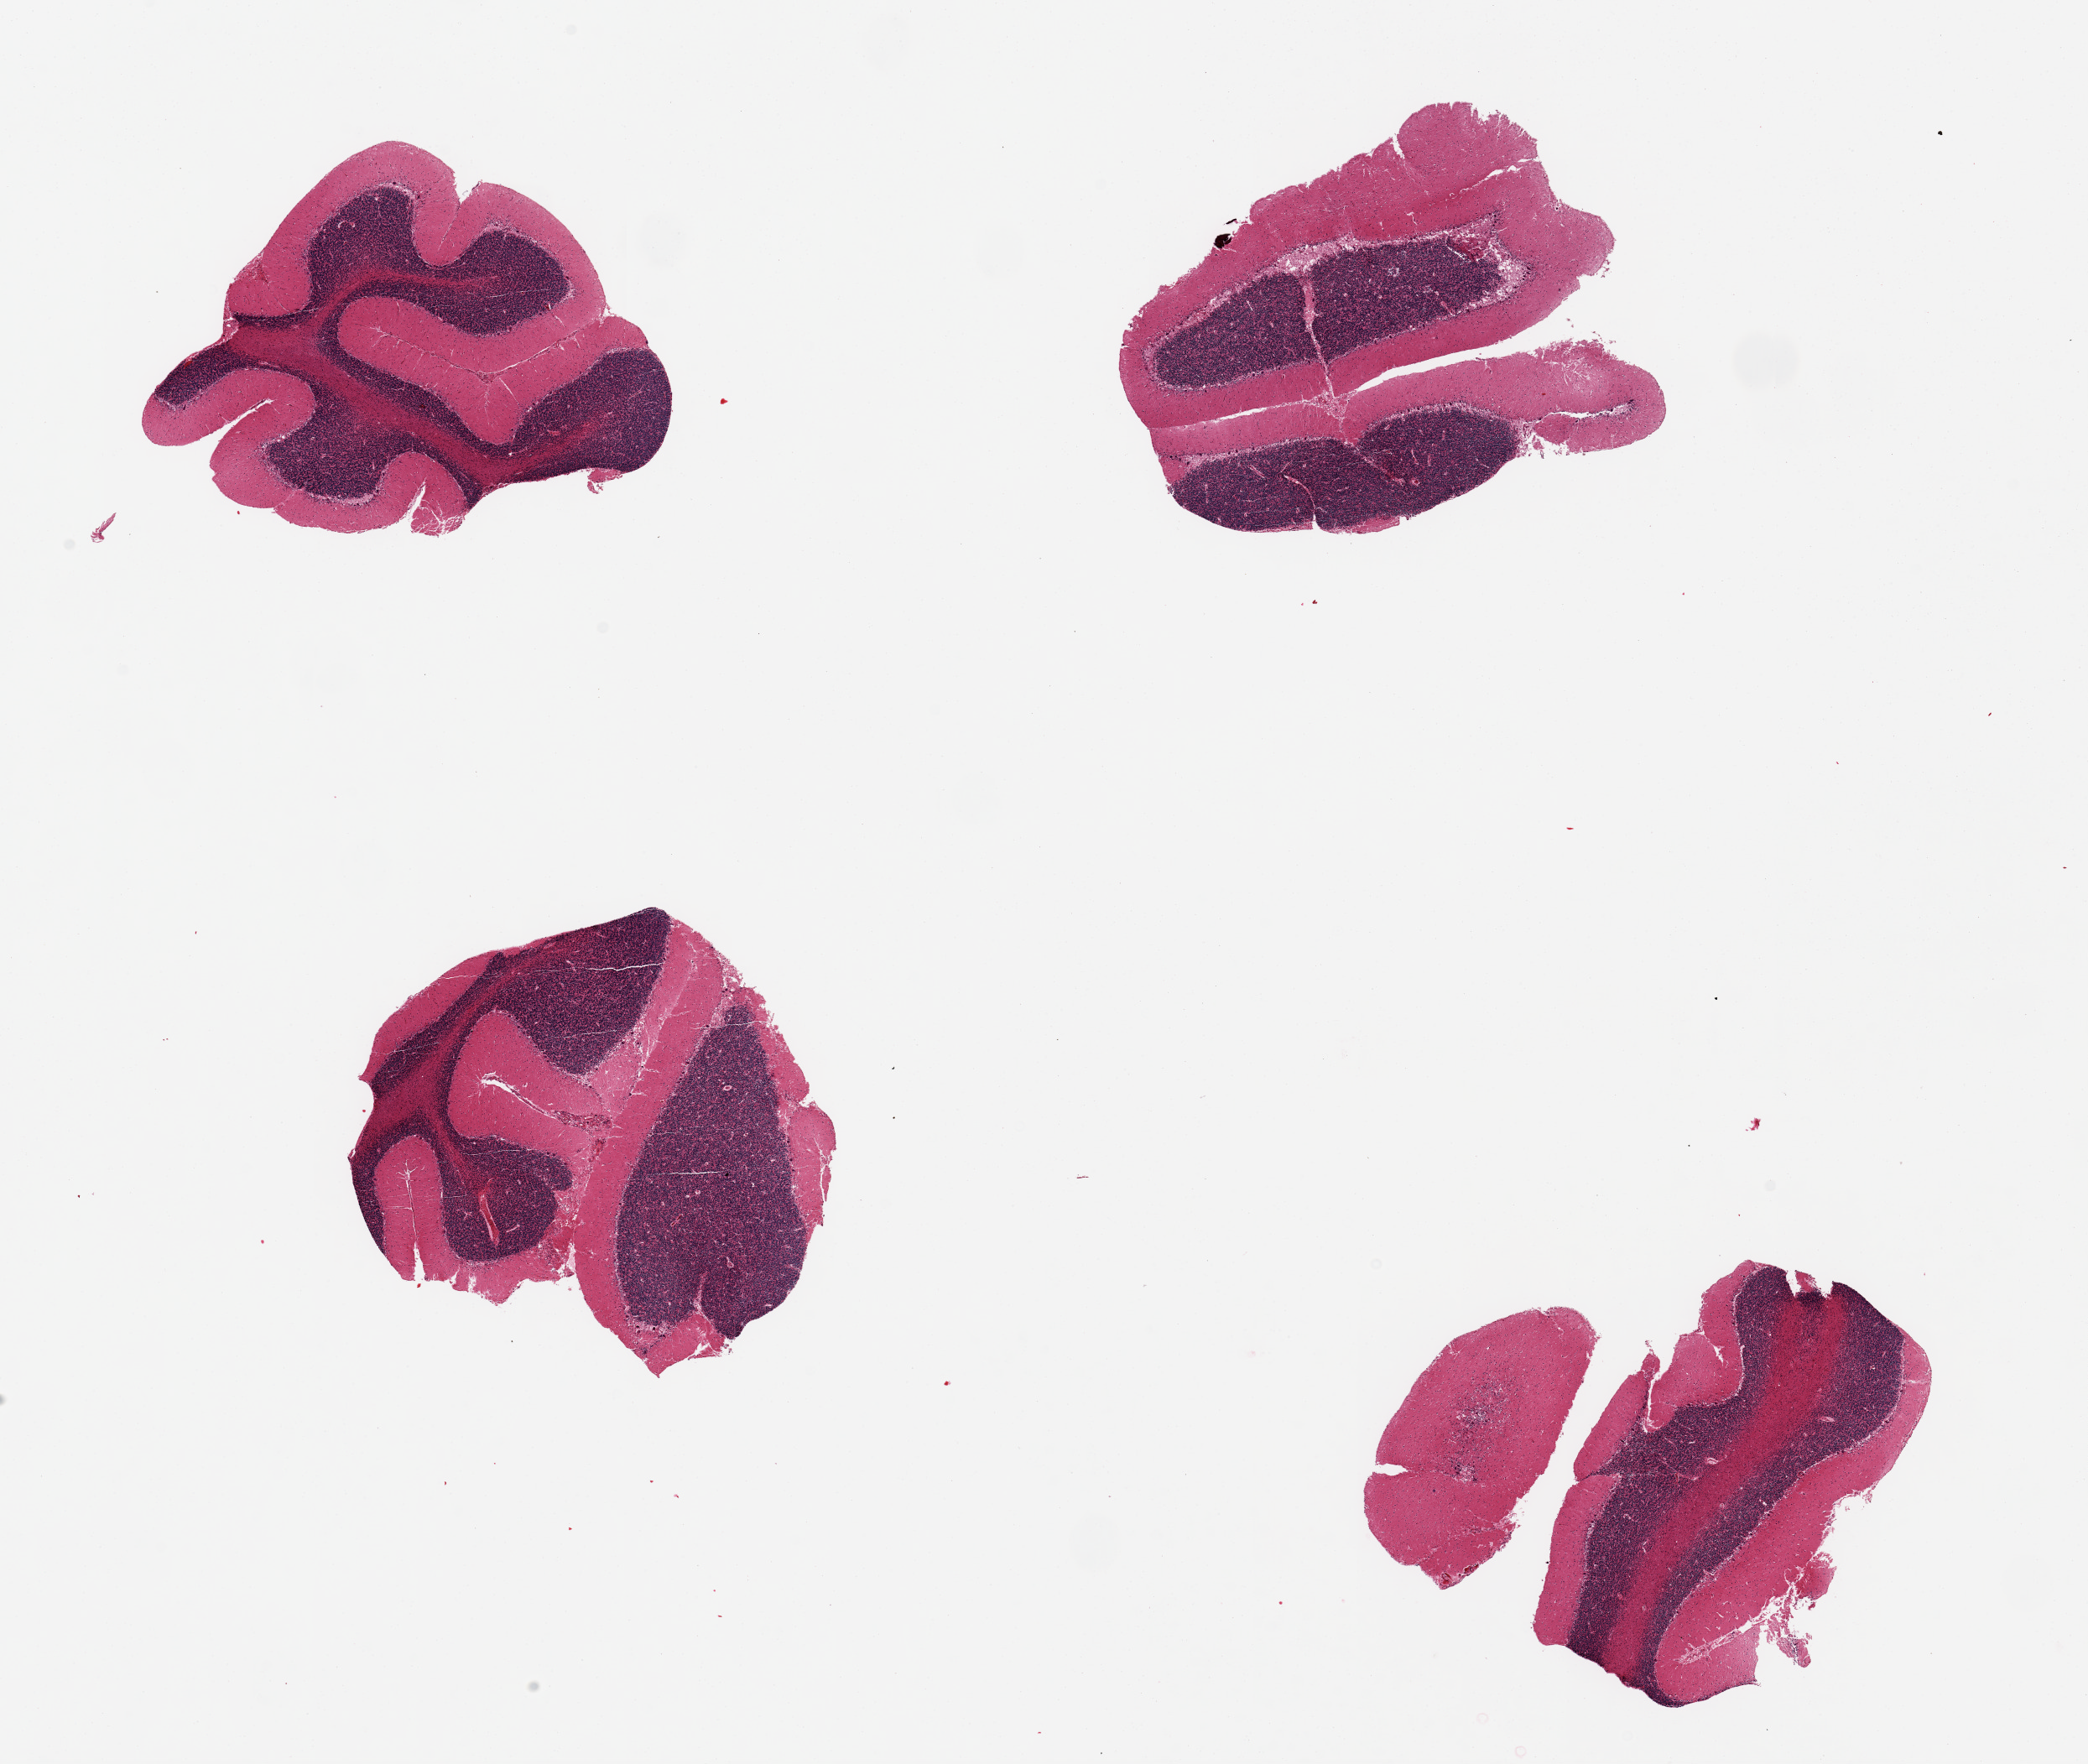
Digitized H&E-stained section — low-resolution overview of the scanned area, about 19.7 x 16.6 mm (from a 20x scan). PAXgene-fixed, paraffin-embedded tissue. Sampled site (target tissue): cerebellum. Donor tissue sample.
Pathologist's review note for this sample: 4 pieces, no abnormalities.